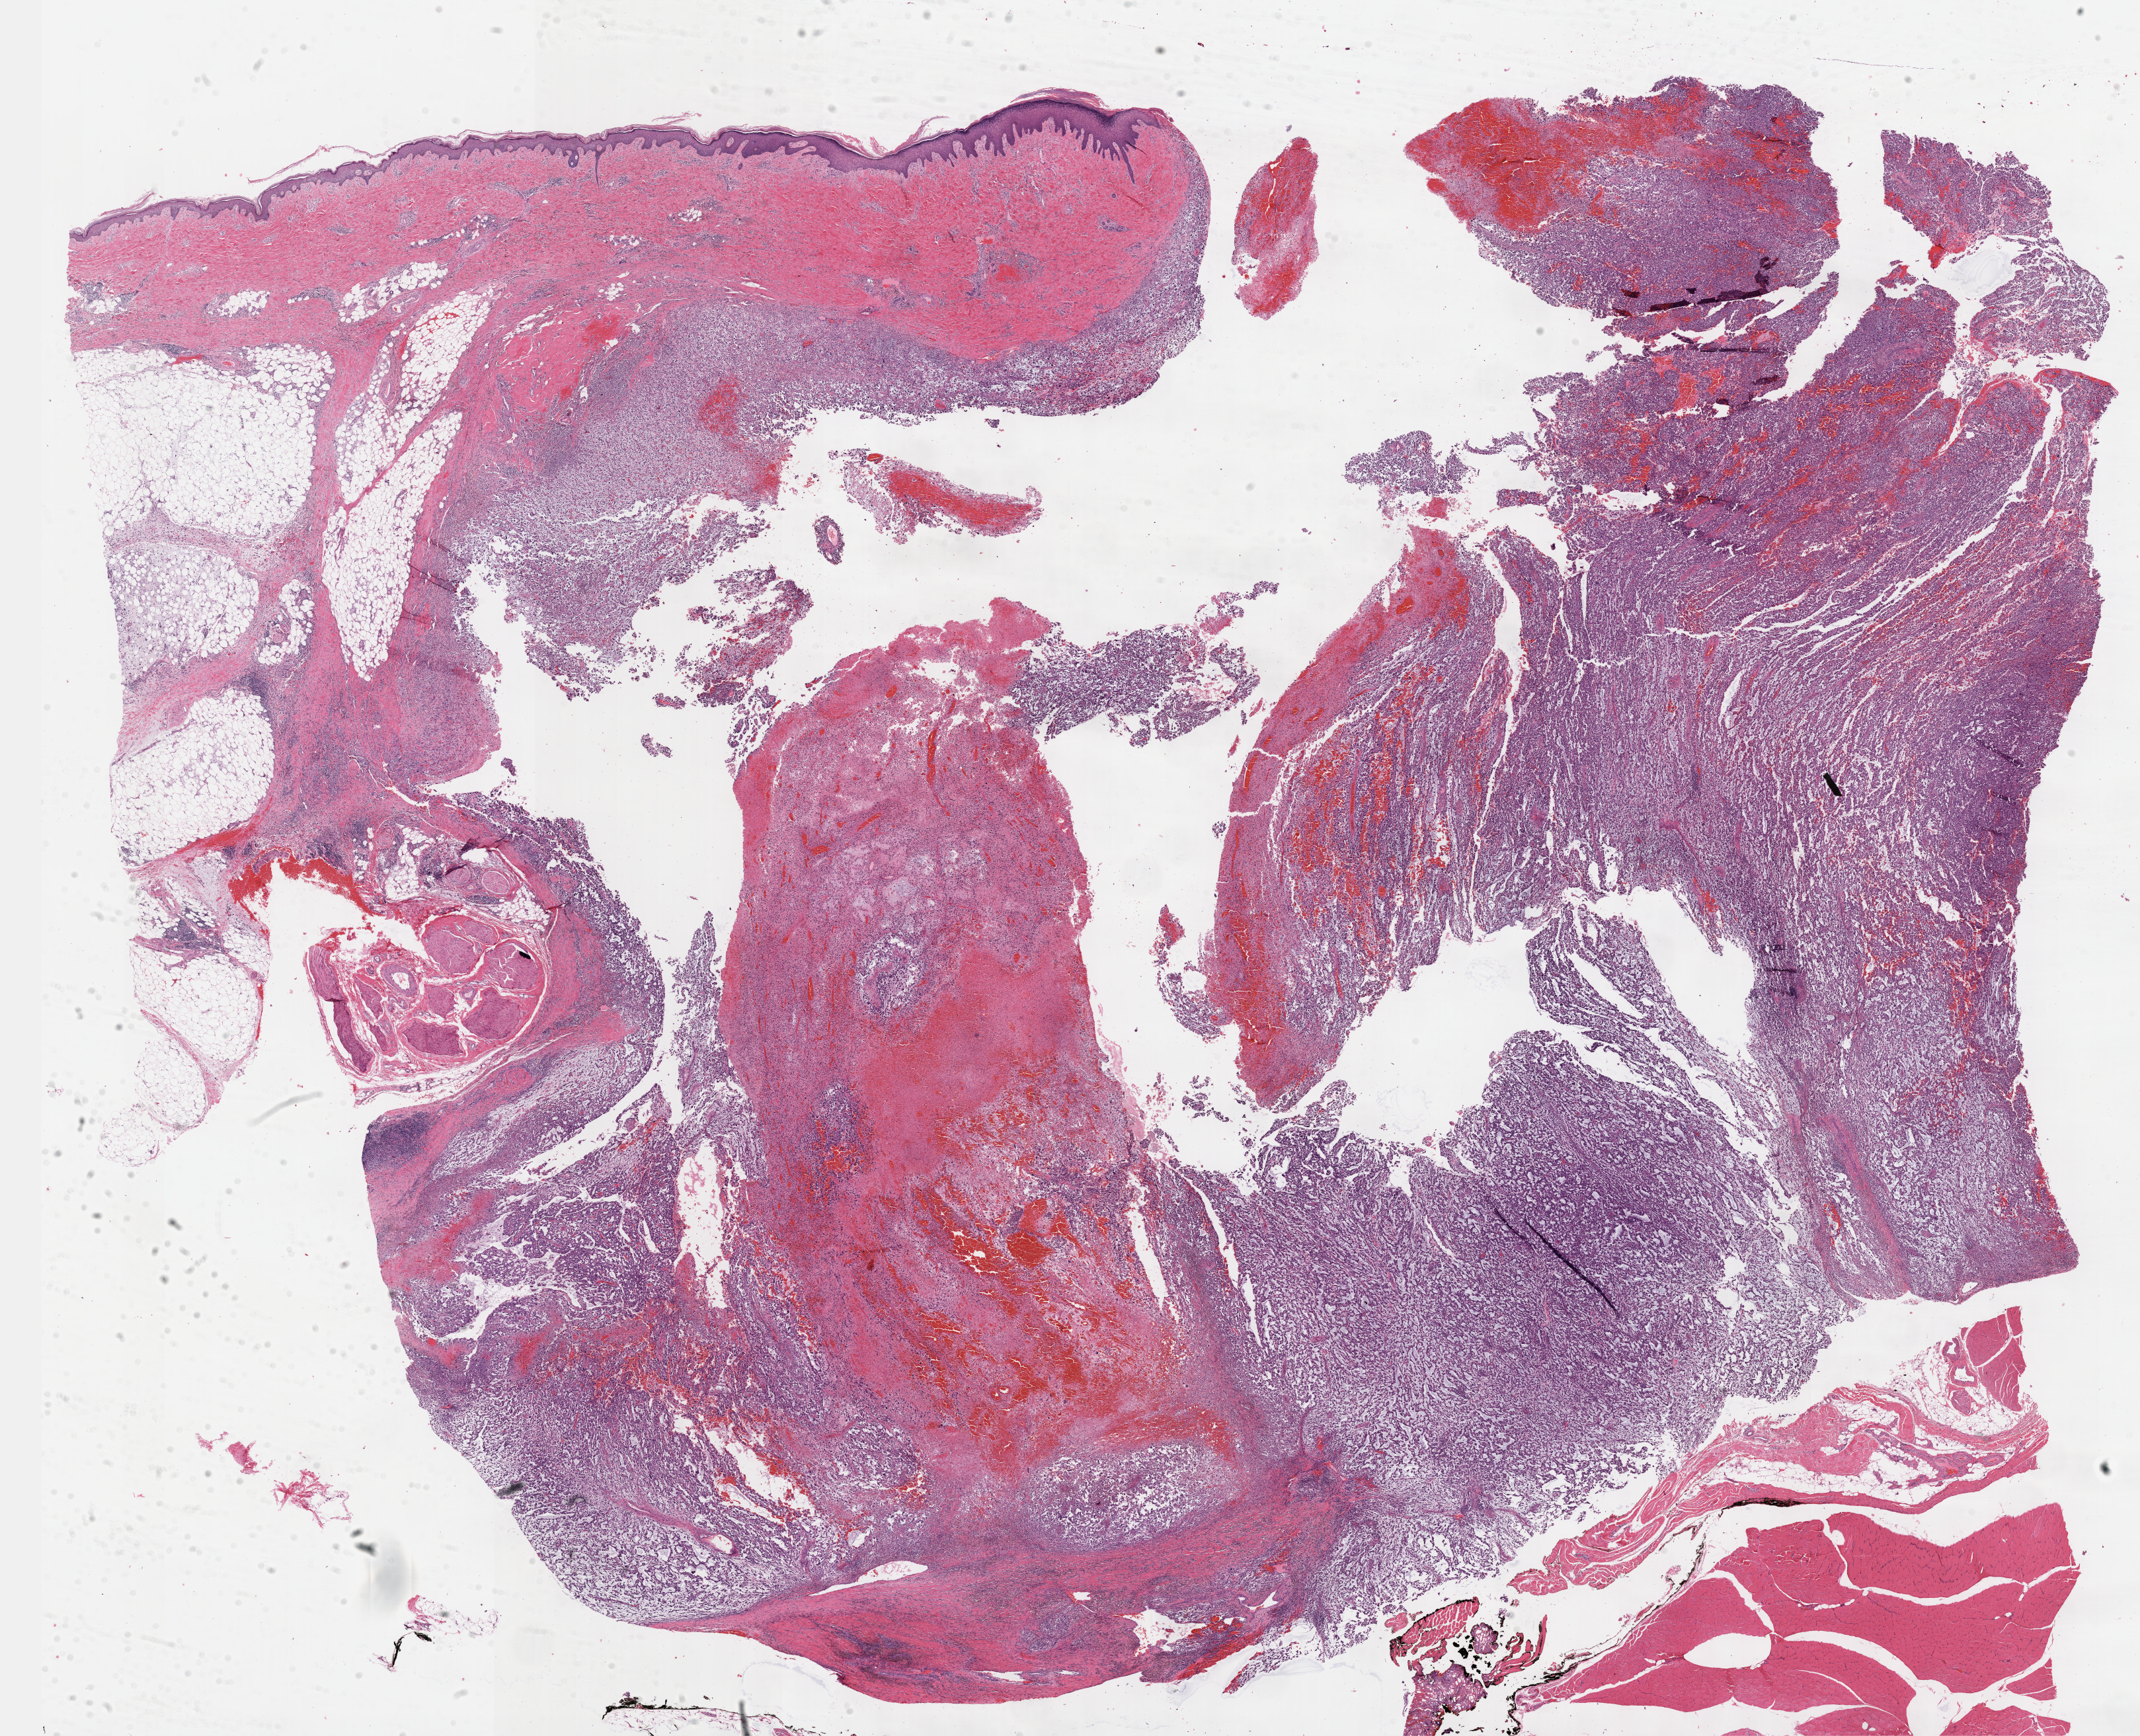
H&E-stained whole-slide image — a low-resolution overview of the entire scanned area, about 26.2 x 21.2 mm (slide scanned at 40x), formalin-fixed paraffin-embedded (FFPE) diagnostic section, sample: primary tumour, connective, subcutaneous and other soft tissues. Female, age 59 years at initial diagnosis.
Pathologic diagnosis: Fibromyxosarcoma (connective, subcutaneous and other soft tissues of lower limb and hip).